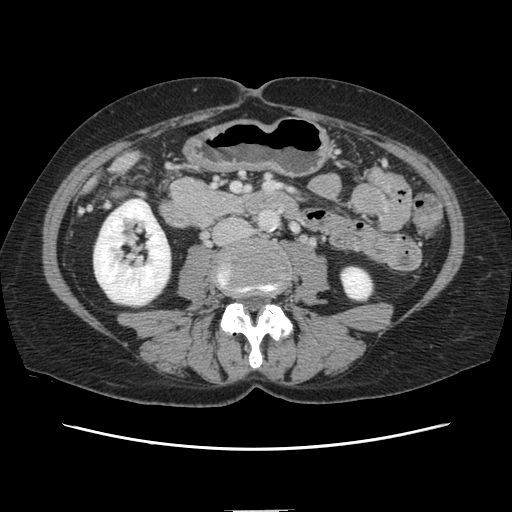
Contrast-enhanced abdominal CT, one axial slice; position 23 of 141 along the scan axis; intravenous contrast given; soft-tissue window (W 400 / L 40 HU); 512 × 512 image matrix, field of view 350 × 350 mm. Female patient, age 63 years. From the clinical record (not read from this slice): diagnosis: colorectal cancer liver metastases, imaged before liver resection; multiple liver metastases: yes; largest metastasis: 3.2 cm; disease in both lobes: yes.
Structures marked on this image (manually delineated by an expert):
- liver: bounding box (x1, y1, x2, y2) in pixels: (118, 160, 130, 168)